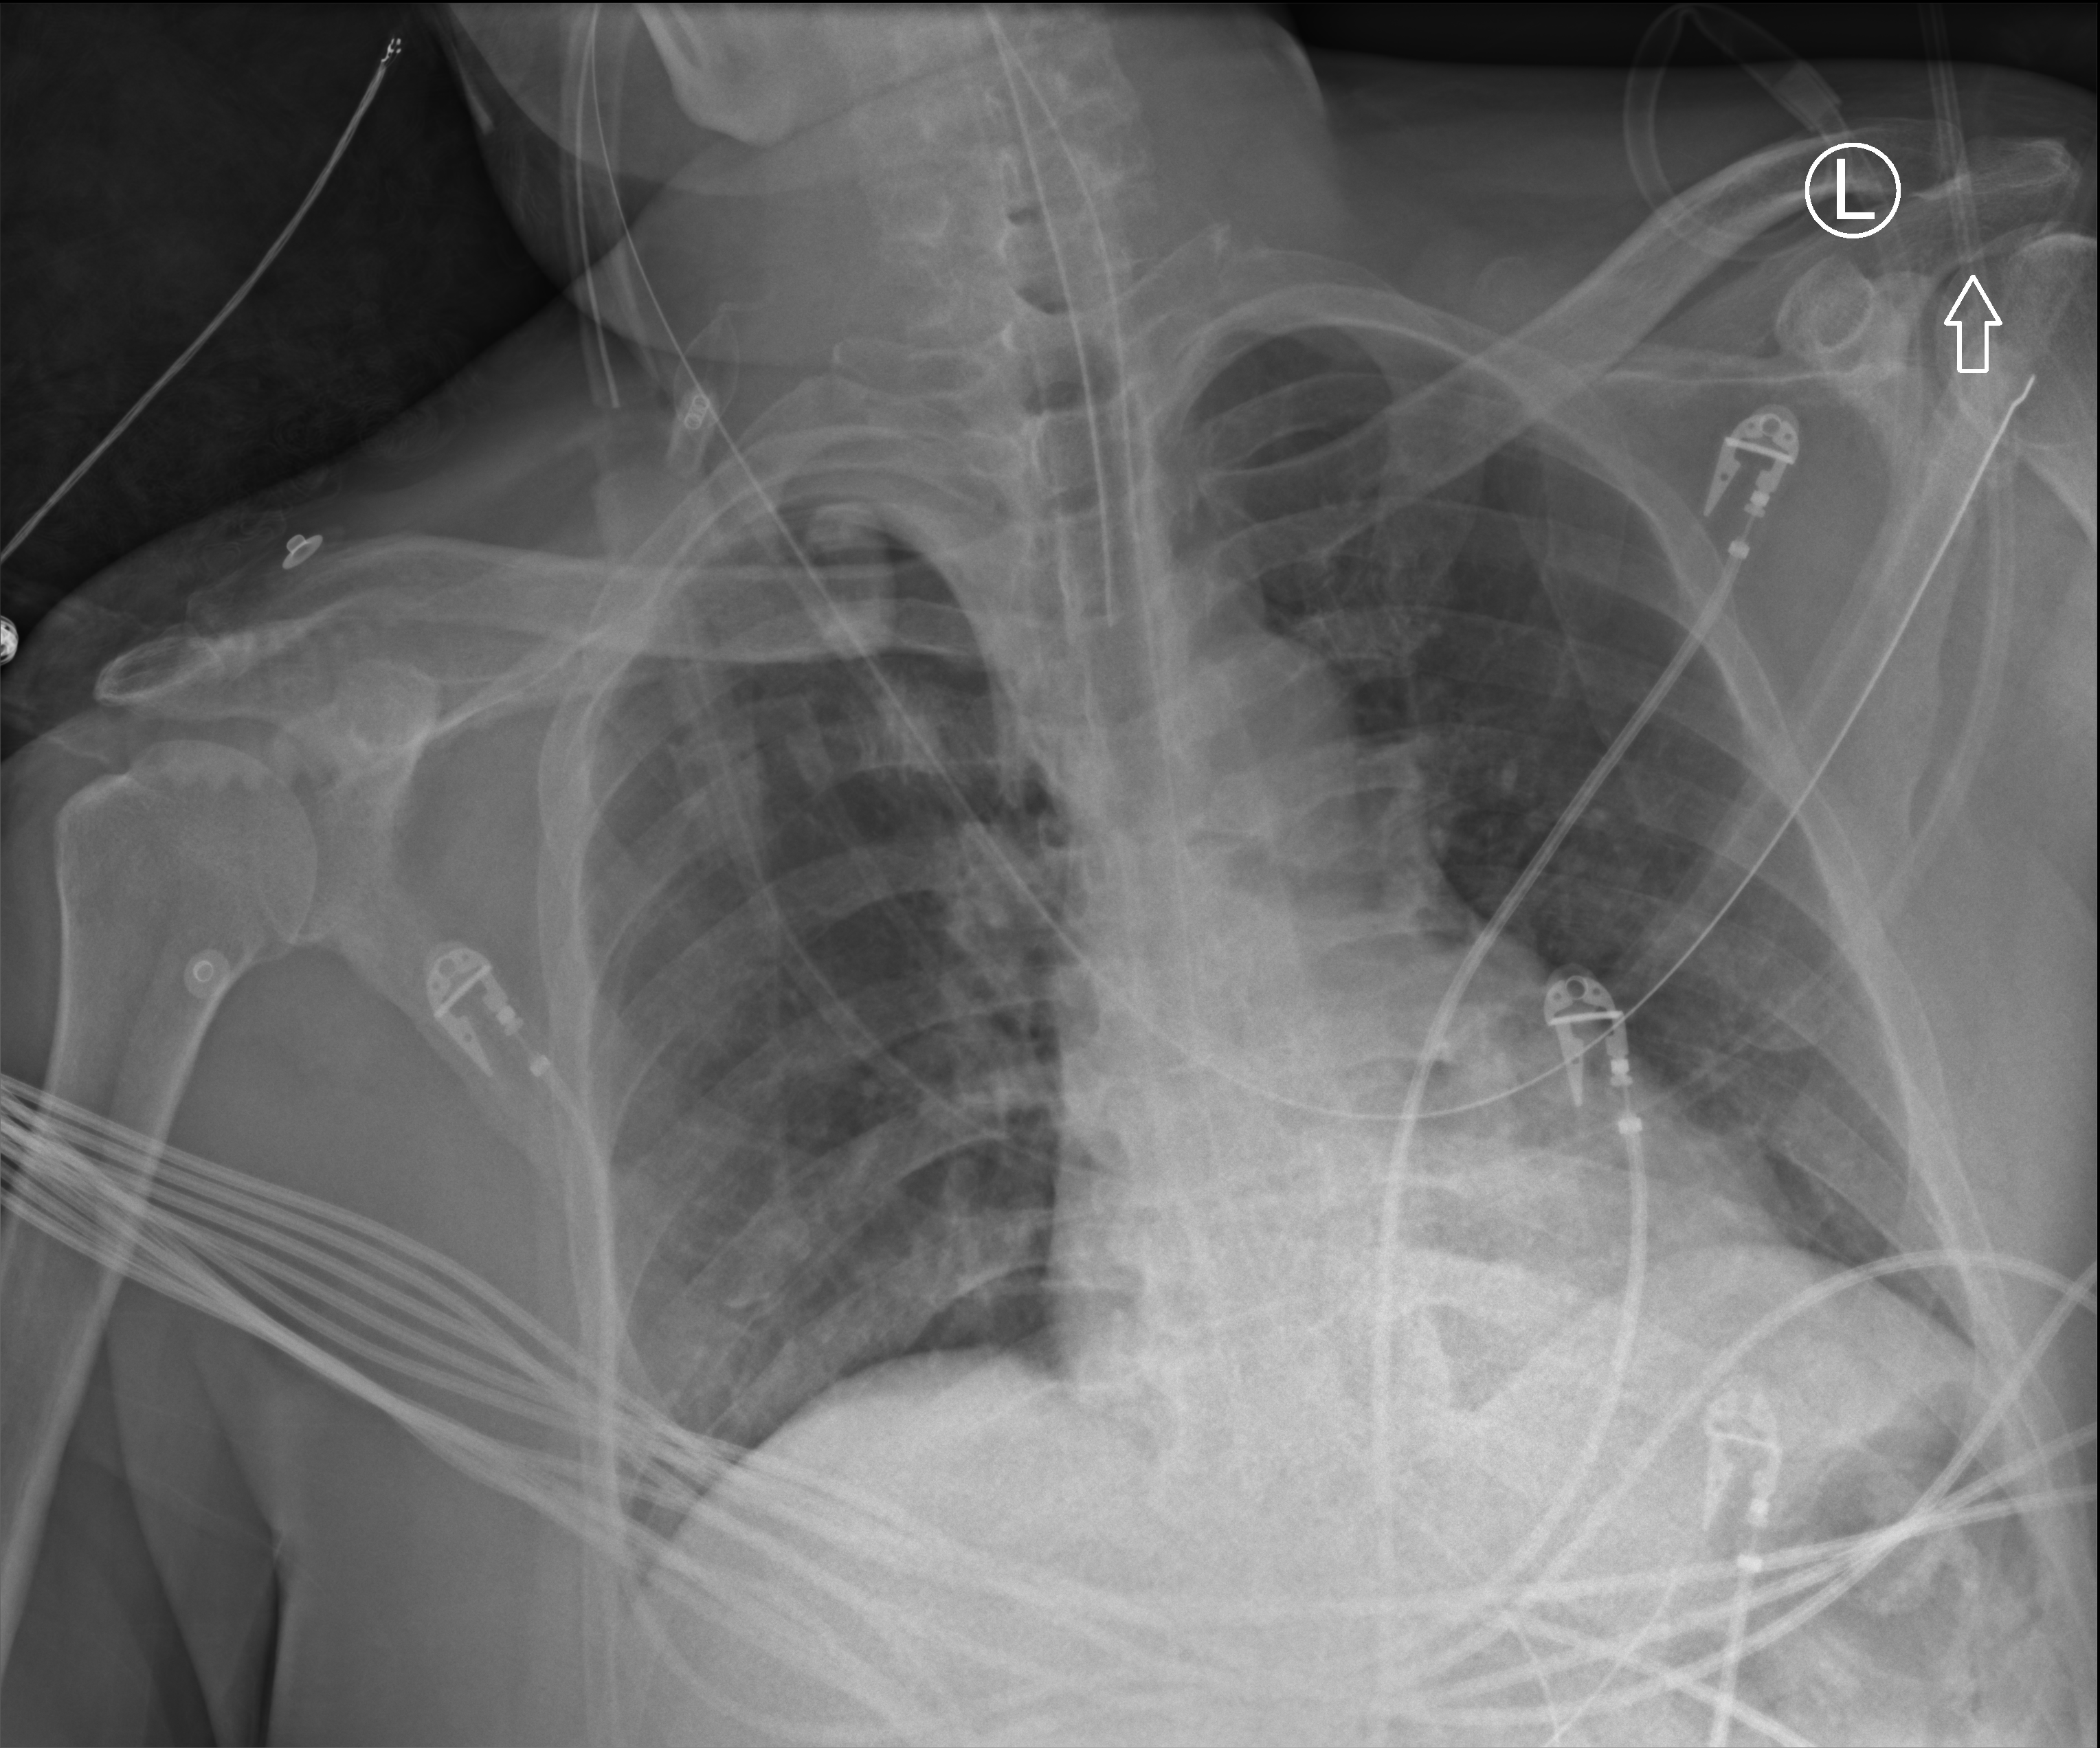
Chest X-ray (portable), anteroposterior (AP) projection. Adult patient hospitalised with COVID-19, age 18–59 years.
Hospital-stay facts (about this admission, not read from this image; timing relative to this image not recorded):
- admitted to intensive care during this hospital stay: yes